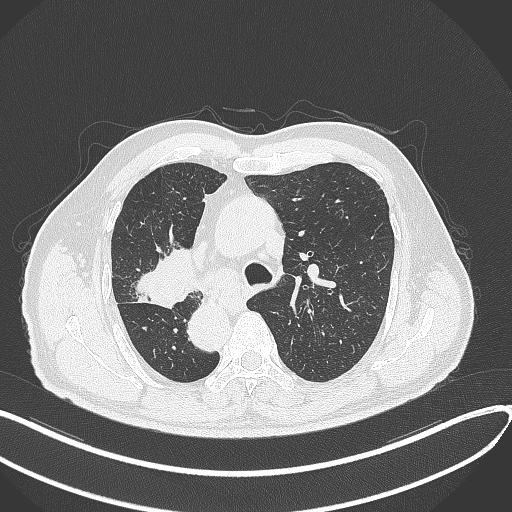
Chest CT, one axial slice; slice 209 of 300 in the series (ordered by position); lung window (W 1500 / L -600 HU); 1 mm slice thickness; 512 × 512 image matrix. Male patient, age 67 years. Case-level facts recorded for this patient, not image findings: clinical TNM (as recorded): T2a N0 M0.
Structures marked on this image (bounding box drawn by a radiologist):
- lung tumour (recorded histology: squamous cell carcinoma): box from (x=133, y=244) to (x=197, y=310) px